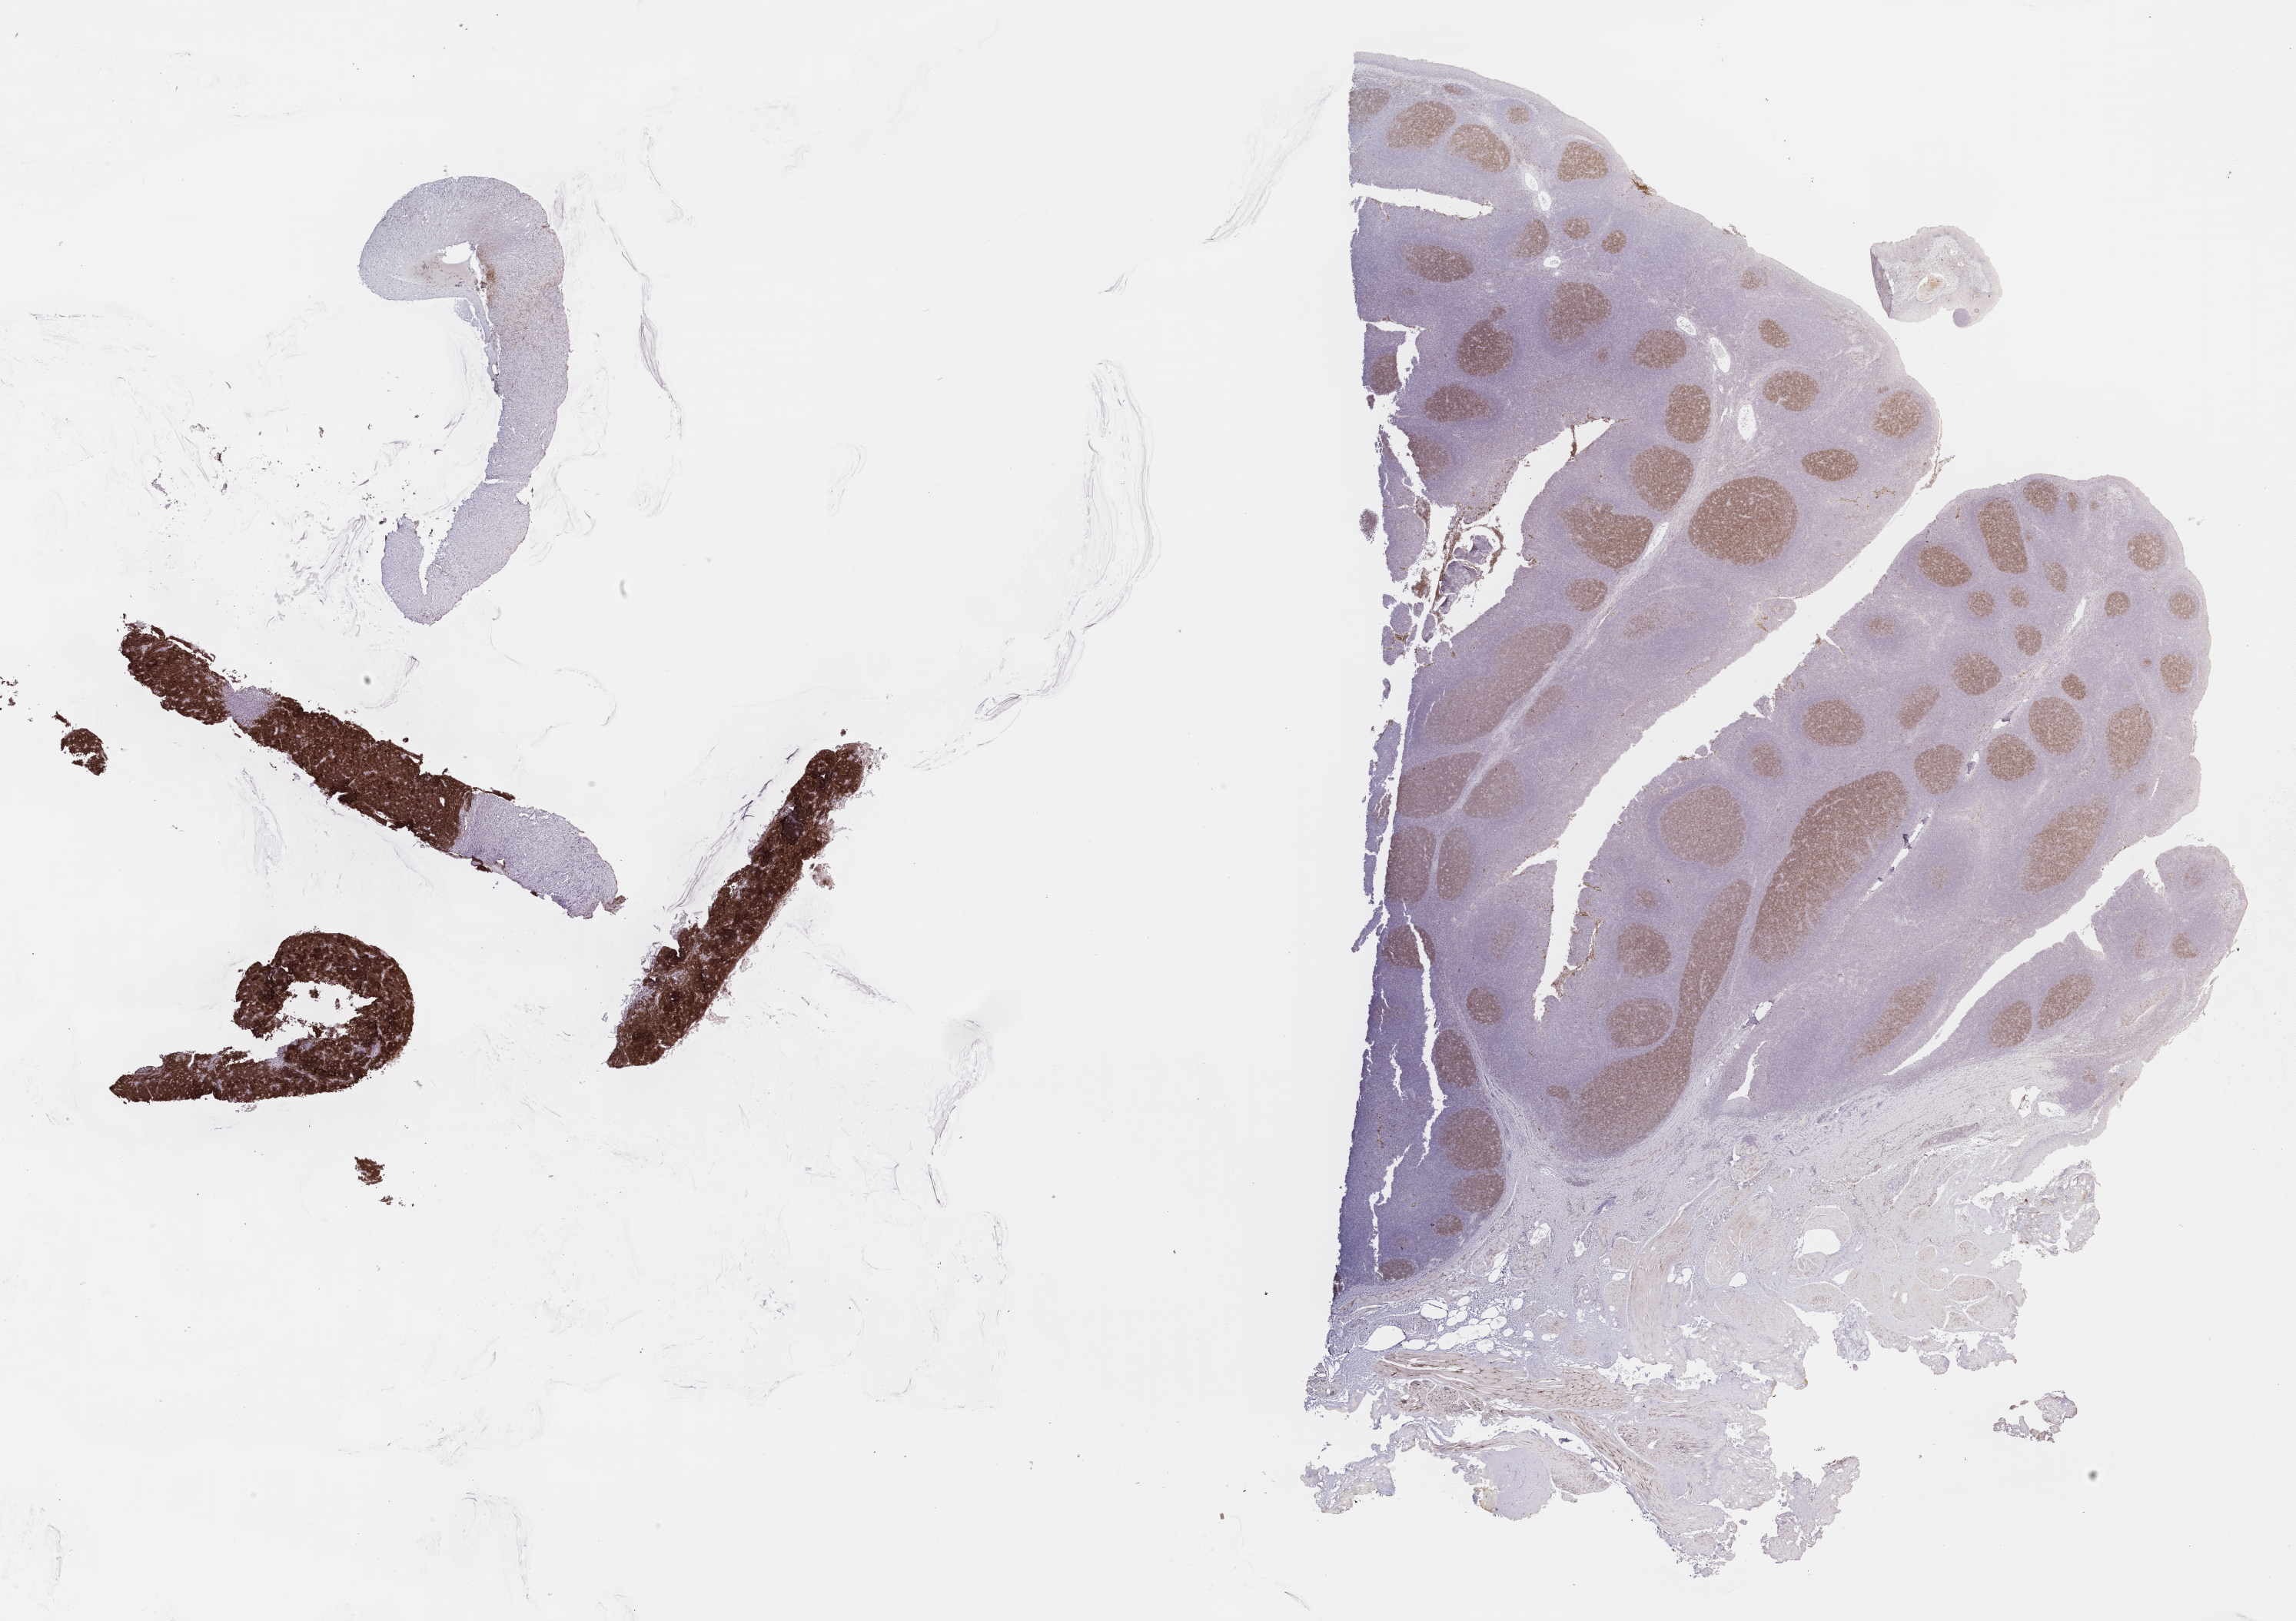
Whole-slide image, immunohistochemical stain for CD10, shown as a low-resolution overview of the whole scanned area (about 24.2 x 17.1 mm). Patient sex: male.
Specimen: tumor tissue.